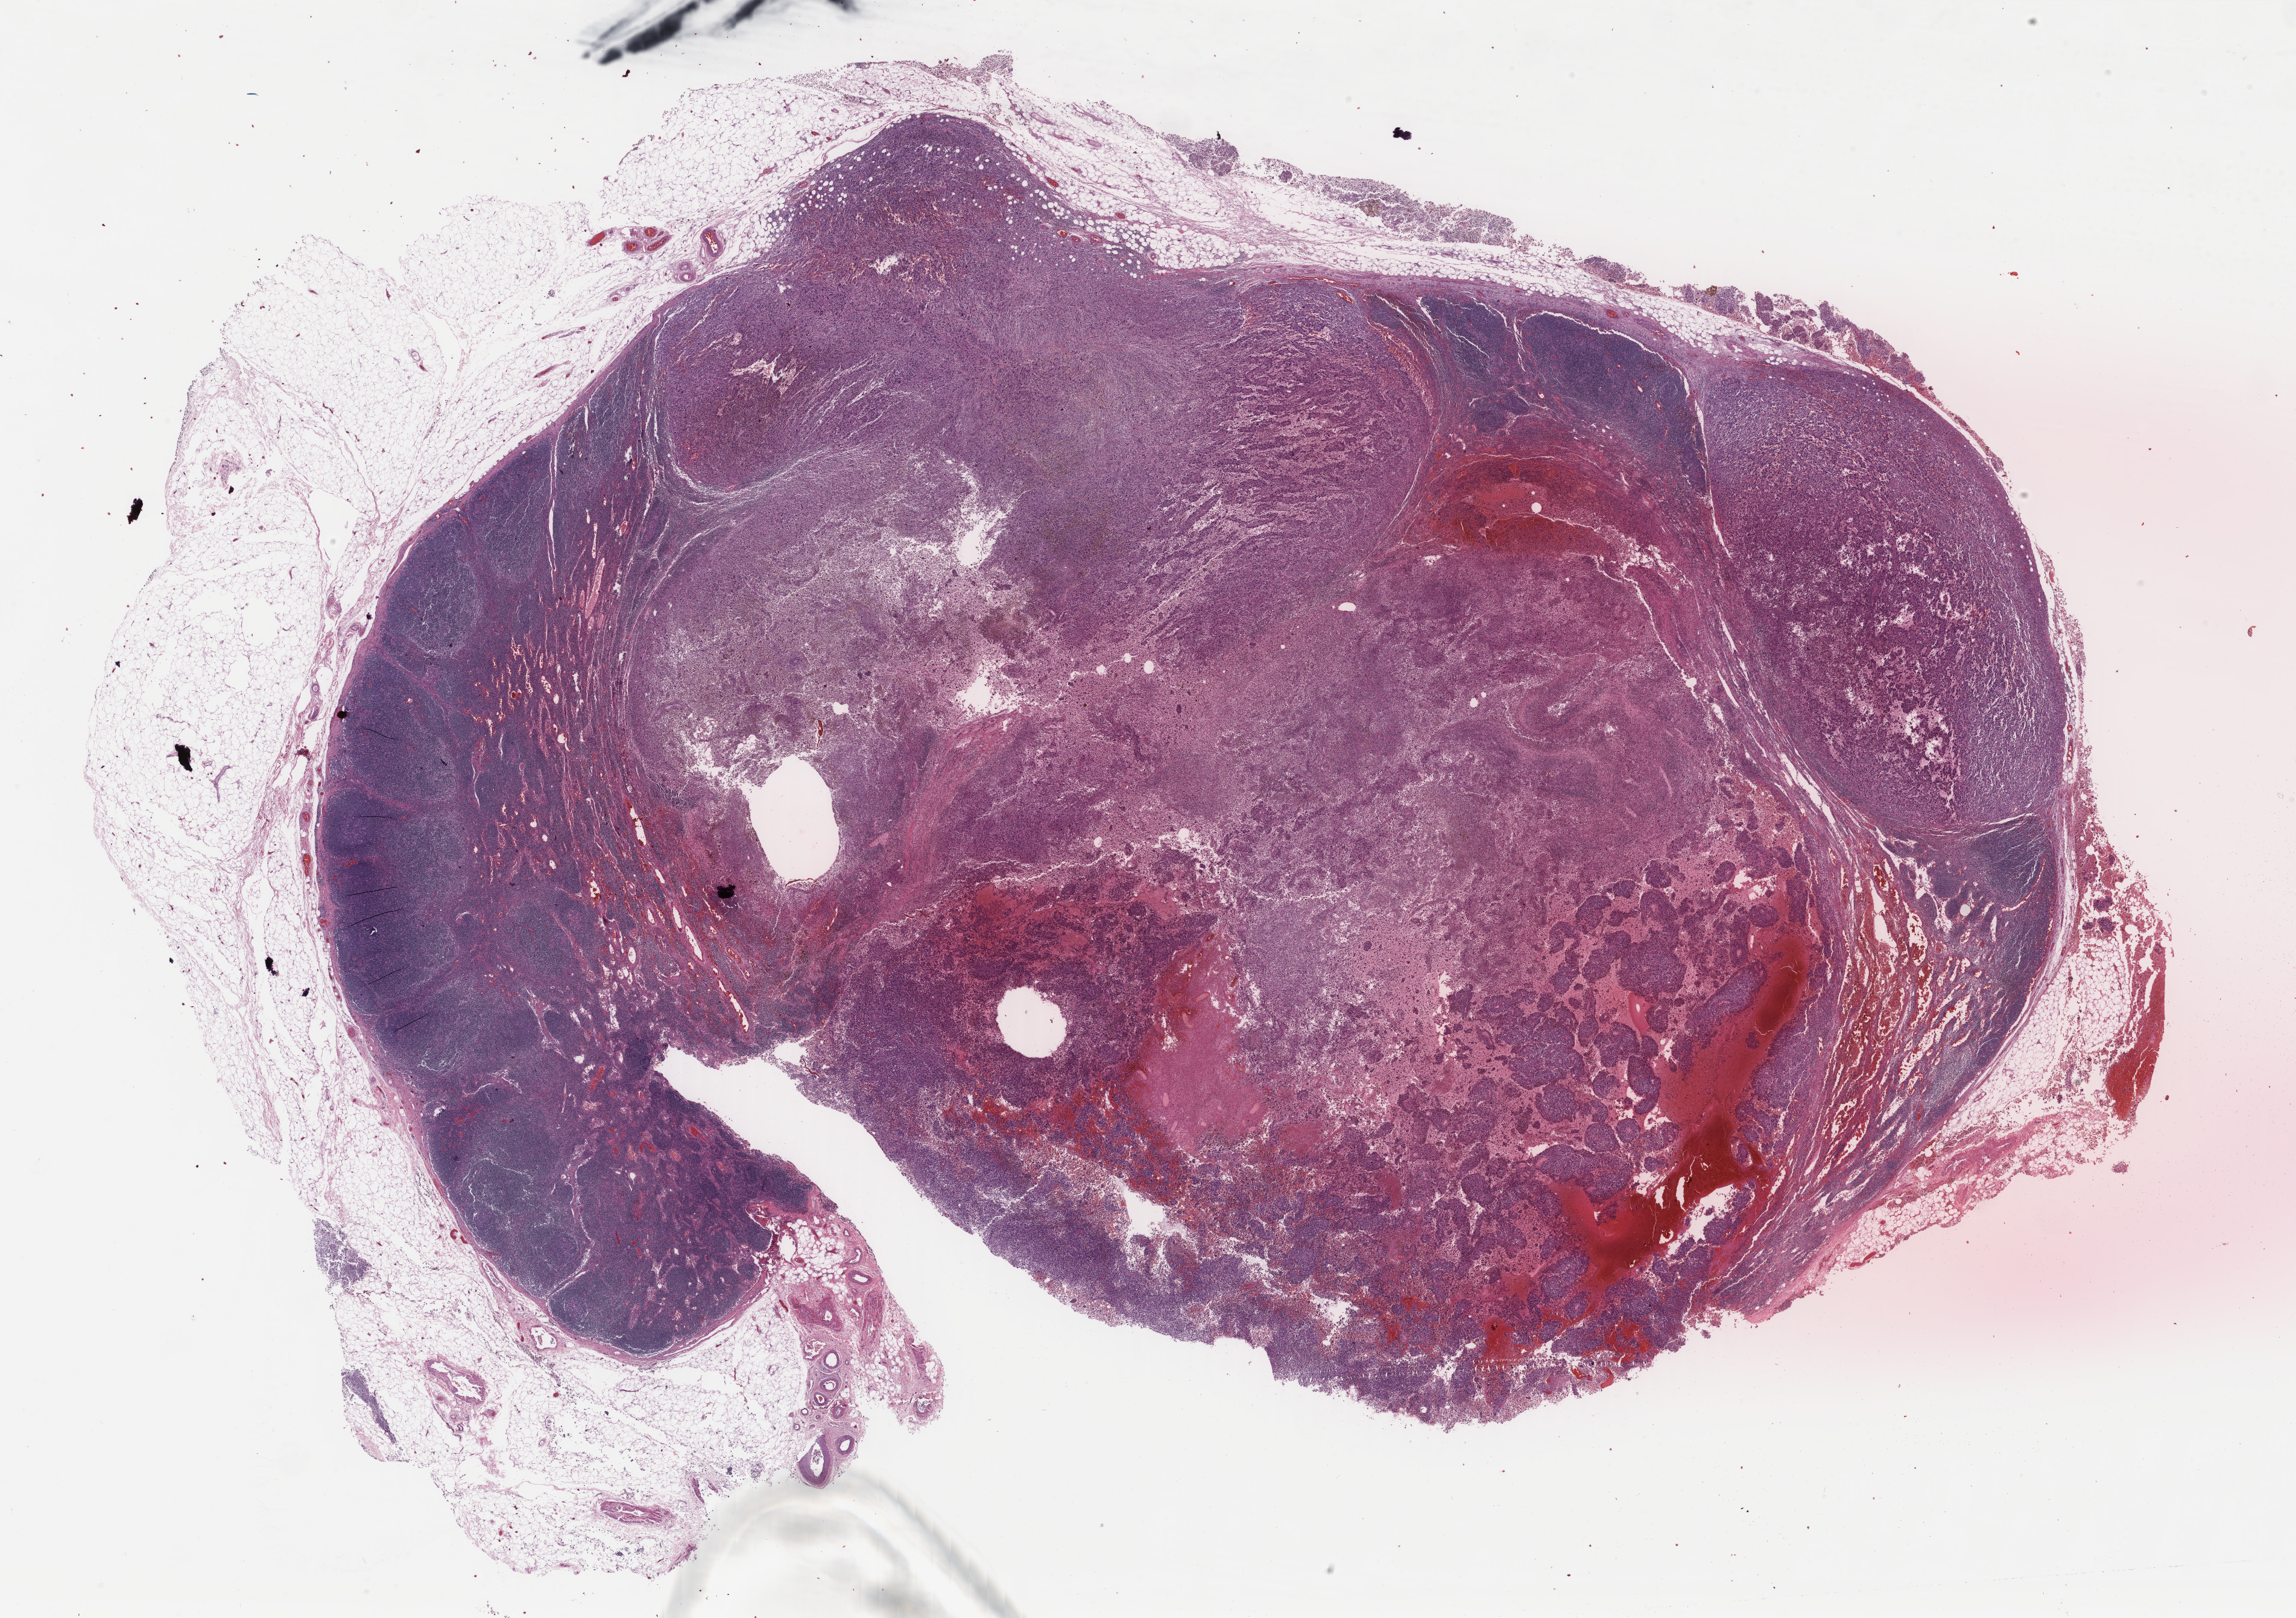
Whole-slide histology image, Hematoxylin and eosin (H&E) stained — shown as a low-resolution overview of the whole scanned area (about 30.2 x 21.3 mm). Formalin-fixed paraffin-embedded (FFPE) diagnostic section. Skin, primary tumour sample. Female patient; age at initial diagnosis 83 years.
Histologic diagnosis: Malignant melanoma, NOS.